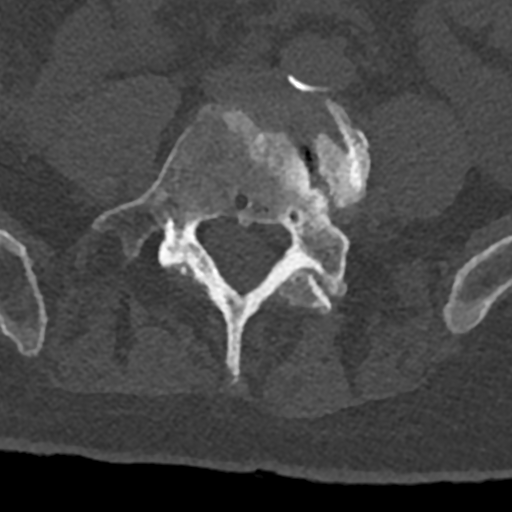
CT including the spine, one axial slice; slice 215 of 797 in the series (ordered by position); 120 kVp; bone window (W 1800 / L 400 HU); 0.5 mm slice thickness; 512 × 512 image matrix, field of view 160 × 160 mm. Male patient, age 74 years. Case-level facts recorded for this patient, not image findings: primary cancer: renal.
Structures marked on this image (semi-automatic segmentation, software-assisted and operator-edited):
- L4 vertebra: bounding box (x1, y1, x2, y2) in pixels: (174, 88, 371, 314)
- L5 vertebra: (93, 106, 348, 374)